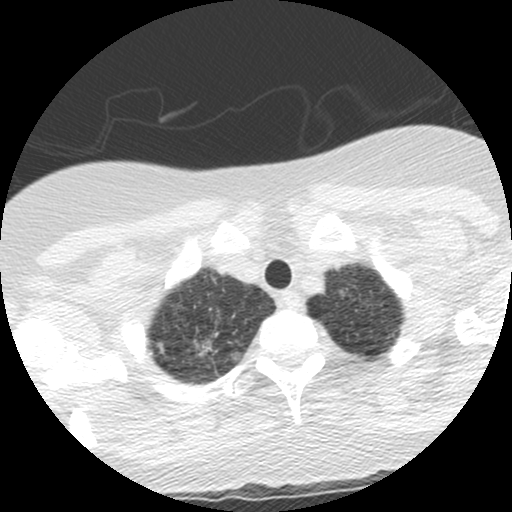
Low-dose screening chest CT, one axial slice. Position 117 of 130 along the scan axis. Reconstruction kernel STANDARD. 120 kVp. Lung window (W 1500 / L -600 HU). 512 × 512 image matrix.
Outlined on this slice (outlined manually by an expert reader):
- lesion 1 (tumor, upper lobe of right lung): bounding box <194,340,212,354> (left, top, right, bottom; pixels)